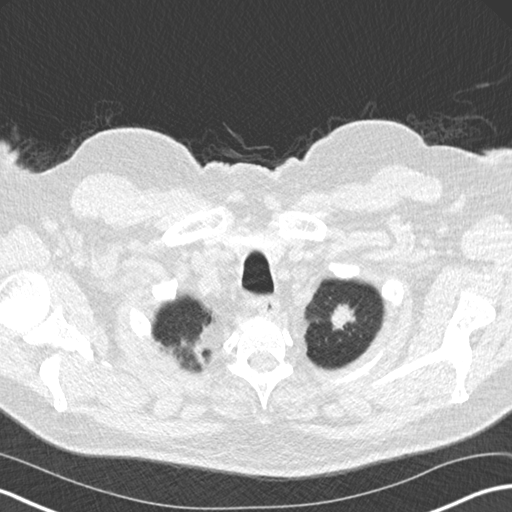
Low-dose screening chest CT, one axial slice; slice 155 of 175 in the series (ordered by position); reconstruction kernel B30f; 120 kVp; lung window (W 1500 / L -600 HU); 2 mm slice thickness; 512 × 512 image matrix.
Structures marked on this image (manually delineated by an expert):
- lesion 1 (tumor, upper lobe of left lung): bounding box <331,304,354,330> (left, top, right, bottom; pixels)